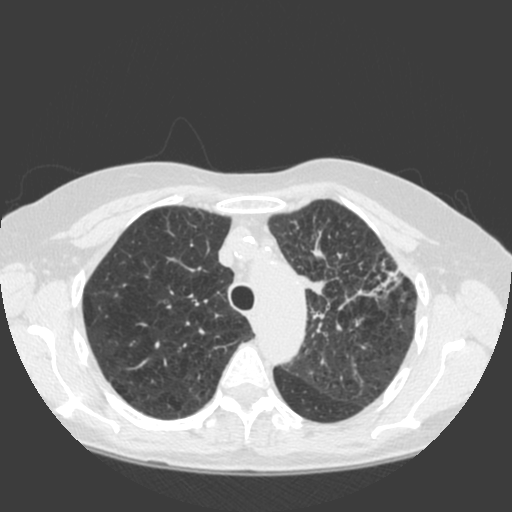
Low-dose screening chest CT, one axial slice. Slice 145 of 184 in the series (ordered by position). Lung window (W 1500 / L -600 HU). 512 × 512 image matrix.
Structures marked on this image (manually delineated by an expert):
- lesion 1 (tumor, hilum of left lung): bounding box <300,273,326,295> (left, top, right, bottom; pixels)